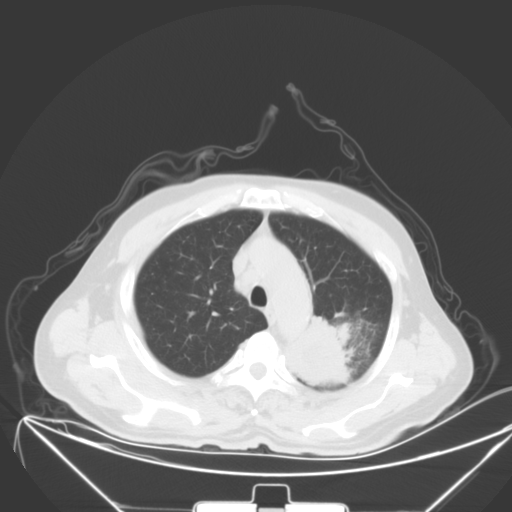
Chest CT, one axial slice. Slice 46 of 64 in the series (ordered by position). 120 kVp. Lung window (W 1500 / L -600 HU). 512 × 512 image matrix, field of view 431 × 431 mm. Male patient, age 58 years. Case-level facts recorded for this patient, not image findings: clinical TNM (as recorded): T2b N3 M1b; histopathological grade: G3.
Structures marked on this image (bounding box drawn by a radiologist):
- lung tumour (recorded histology: adenocarcinoma): bounding box <290,315,359,393> (left, top, right, bottom; pixels)